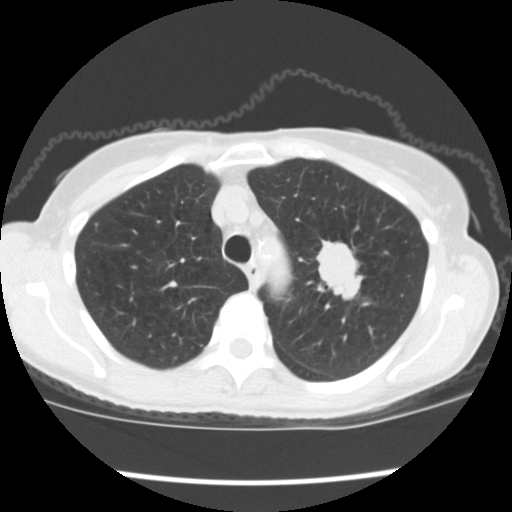
Axial slice from a low-dose chest CT screening exam. Baseline screening round. Lung window (W 1500 / L -600 HU). 2.5 mm slice thickness. Slice 36 of 176 in the series. 512 × 512 image matrix, field of view 318 × 318 mm. Female participant, aged 67 years at enrolment.
Lesion marked by an expert reader, bounding box [x1, y1, x2, y2] px = [306, 235, 379, 311]. Reader record for this screening exam (exam-level; its link to the box is not recorded): non-calcified nodule or mass ≥4 mm, left upper lobe, 34 × 32 mm, spiculated (stellate) margins, soft tissue attenuation, pre-existing on the prior screen: no. Participant outcome: lung cancer diagnosed 17 days after this screen — small cell carcinoma, NOS, left upper lobe, stage IIIA (AJCC 6th edition), 40 mm at pathology.